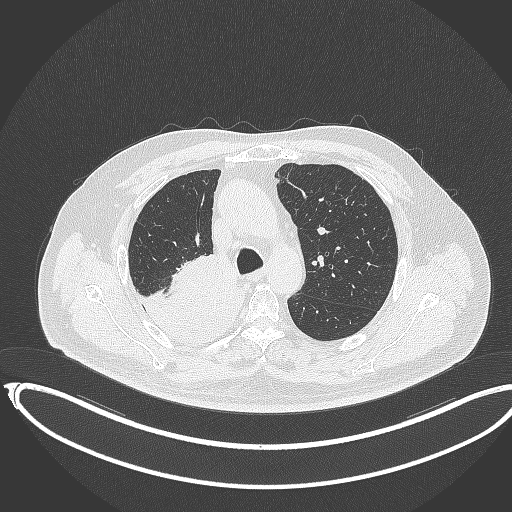
Chest CT, one axial slice; position 255 of 403 along the scan axis; lung window (W 1500 / L -600 HU); 512 × 512 image matrix, field of view 436 × 436 mm. Male patient, age 68 years. Case-level facts recorded for this patient, not image findings: clinical TNM (as recorded): T2a N0 M0.
Structures marked on this image (rectangle marked by the reading radiologist):
- lung tumour (recorded histology: adenocarcinoma): box from (x=128, y=260) to (x=239, y=344) px